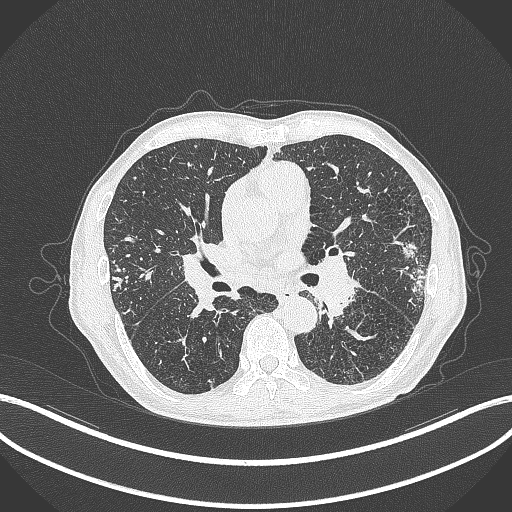
Chest CT, one axial slice. Position 217 of 463 along the scan axis. 120 kVp. Lung window (W 1500 / L -600 HU). 1 mm slice thickness. 512 × 512 image matrix. Male patient, age 74 years. From the clinical record (not read from this slice): clinical TNM (as recorded): T2a N1 M0.
Annotated regions visible in this slice (rectangle marked by the reading radiologist):
- lung tumour (recorded histology: adenocarcinoma): bounding box (x1, y1, x2, y2) in pixels: (398, 239, 420, 265)